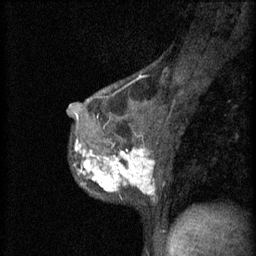
Breast MRI (dynamic contrast-enhanced), one sagittal slice; slice 36 of 60 in the series (ordered by position); 3 images stored at this slice position (order not interpretable as contrast timing); 1.5 T; TE 4.2 ms, TR 11 ms; 256 × 256 image matrix, field of view 180 × 180 mm. Patient: female, 37 years.
Structures marked on this image (semi-automatic segmentation, software-assisted and operator-edited):
- analysis volume of interest (the breast-tissue region the enhancement analysis was run in; not a lesion): bounding box (x1, y1, x2, y2) in pixels: (72, 138, 163, 199)
- tumour enhancement mask (voxels above the 70 % enhancement threshold inside the analysis volume of interest): (75, 142, 155, 195)